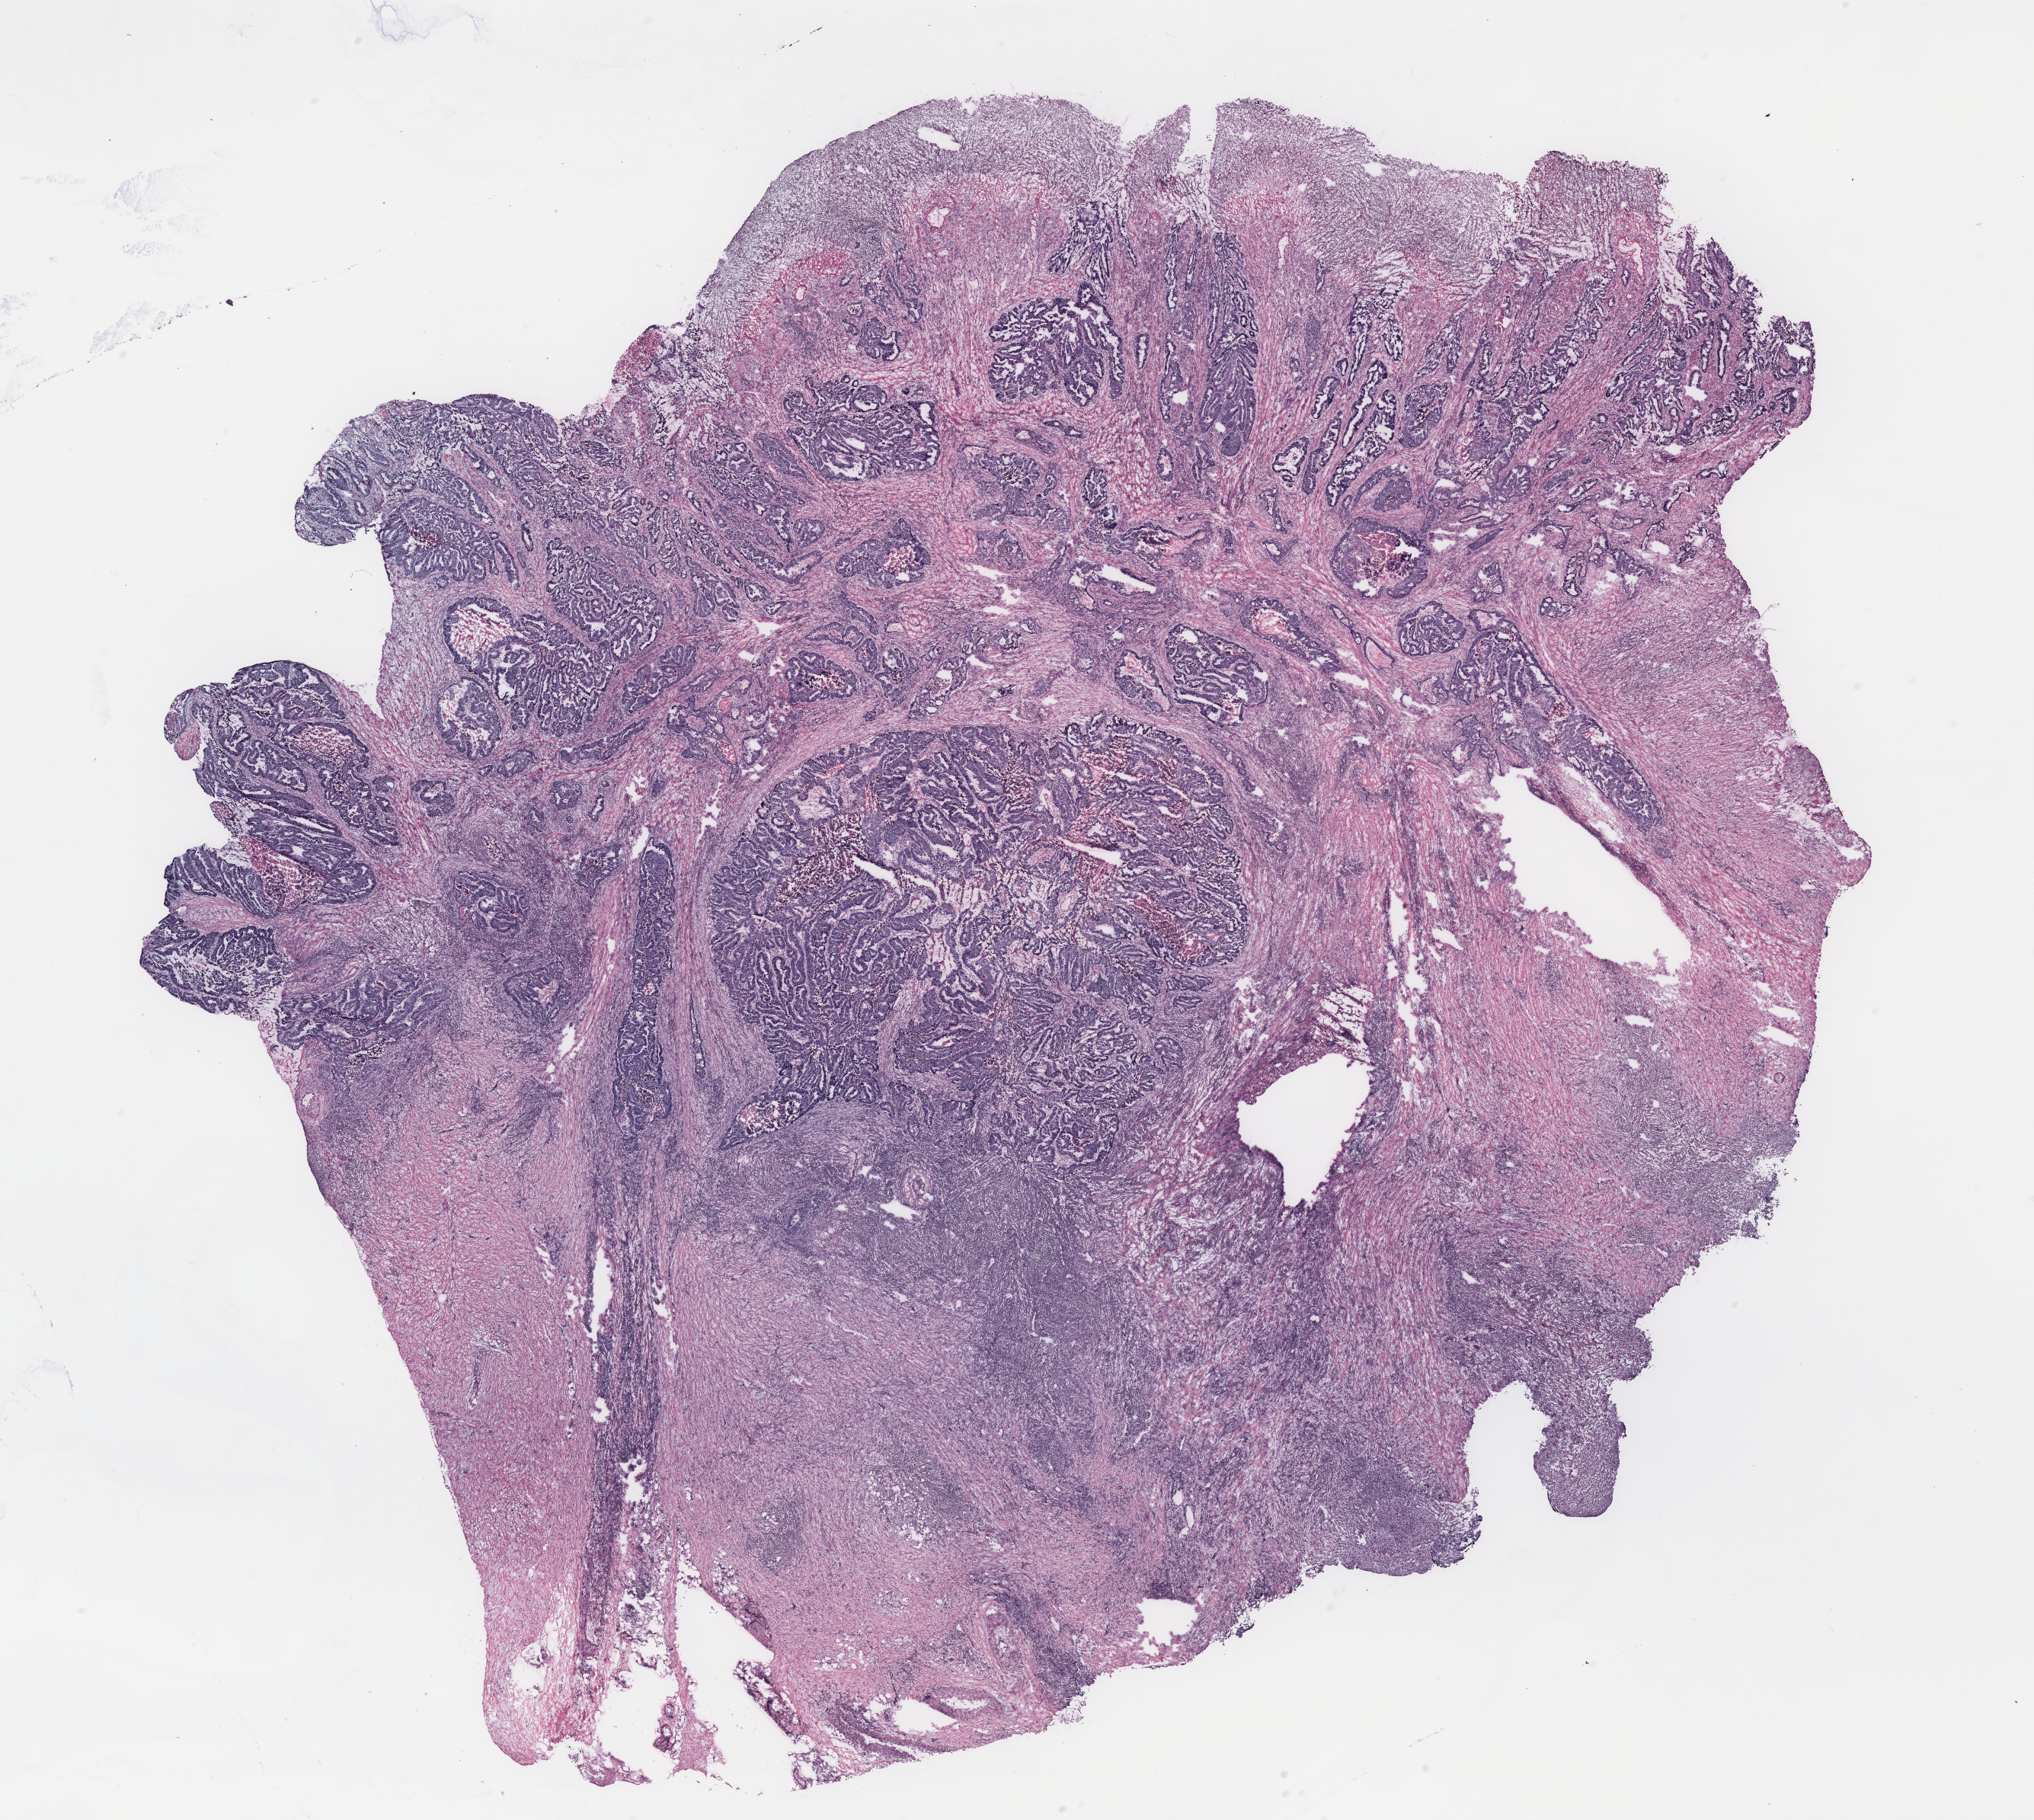
Whole-slide histology image, Hematoxylin and eosin (H&E) stained — a low-resolution overview of the entire scanned area, about 21.4 x 19.1 mm; colon, tissue type not recorded.
* patient diagnosis (cohort enrolment): colon cancer (colon)